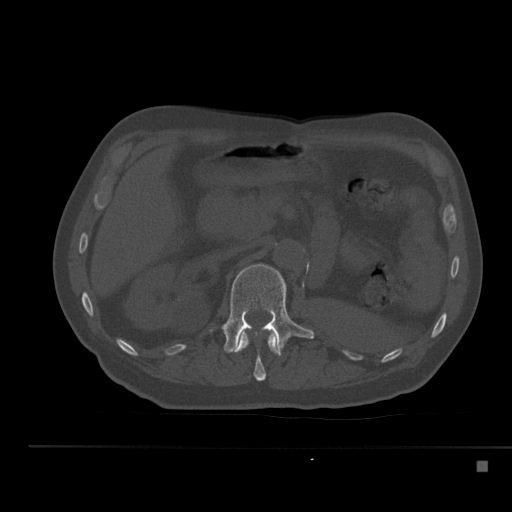
CT including the spine, one axial slice. Position 212 of 517 along the scan axis. Reconstruction kernel Br40s. Bone window (W 1800 / L 400 HU). 1.5 mm slice thickness. 512 × 512 image matrix, field of view 408 × 408 mm. Male patient, age 70 years. From the clinical record (not read from this slice): primary cancer: renal; vertebrae with lytic lesions (as recorded): T4, T6, T10, T12, L3, L4, L5.
Structures marked on this image (semi-automatically segmented with operator editing):
- L1 vertebra: bounding box <222,264,314,355> (left, top, right, bottom; pixels)
- T12 vertebra: <231,332,280,381>